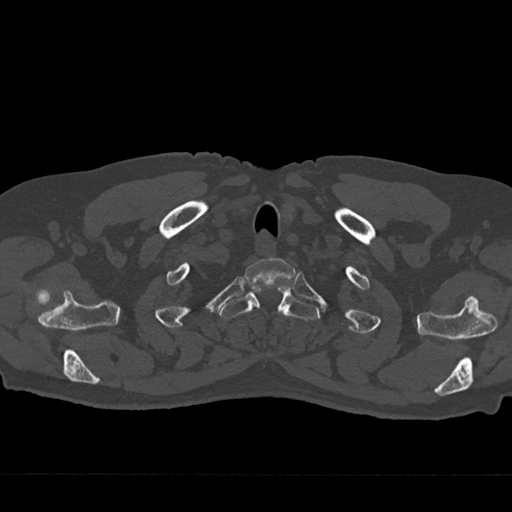
CT including the spine, one axial slice. Slice 629 of 797 in the series (ordered by position). 120 kVp. Bone window (W 1800 / L 400 HU). 512 × 512 image matrix. Male patient, age 75 years. From the clinical record (not read from this slice): primary cancer: renal; vertebrae with lytic lesions (as recorded): T4.
Annotated regions visible in this slice (semi-automatic segmentation, software-assisted and operator-edited):
- T1 vertebra: bounding box <244,258,294,286> (left, top, right, bottom; pixels)
- T2 vertebra: <220,288,319,320>